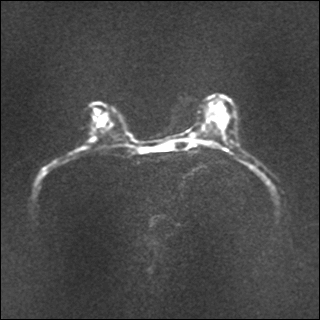
Breast MRI, one axial slice. Position 19 of 35 along the scan axis. Diffusion-weighted series; image 2 of 4 stored at this slice position (different b-values; order by instance number). 1.5 T. 4 mm slice thickness. 320 × 320 image matrix, field of view 320 × 320 mm. Female patient.
Outlined on this slice (expert manual segmentation):
- tumour on diffusion-weighted imaging: bounding box <99,117,104,125> (left, top, right, bottom; pixels)